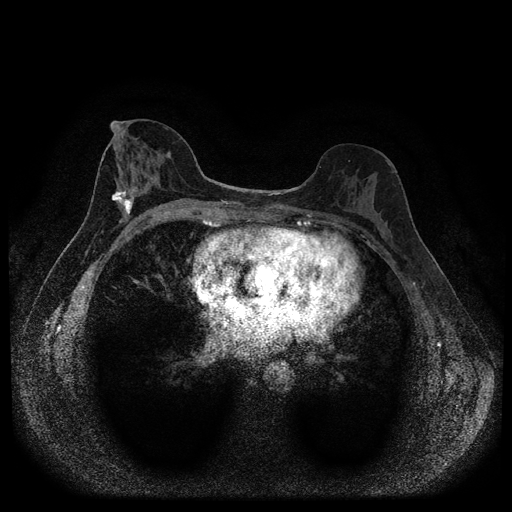
Breast MRI (dynamic contrast-enhanced, multi-phase), one axial slice. Slice 48 of 116 in the series (ordered by position). Dynamic contrast-enhanced series, time point 2 of 5 at this slice position (early post-contrast). 1.5 T. TE 2.7 ms, TR 5.4 ms. 512 × 512 image matrix, field of view 330 × 330 mm. Female patient, age 49 years.
Structures marked on this image (semi-automatic segmentation, software-assisted and operator-edited):
- breast lesion (labelled 'tumour' in the annotation; benign lesions carry a separate 'benign' label): bounding box <110,187,139,219> (left, top, right, bottom; pixels)